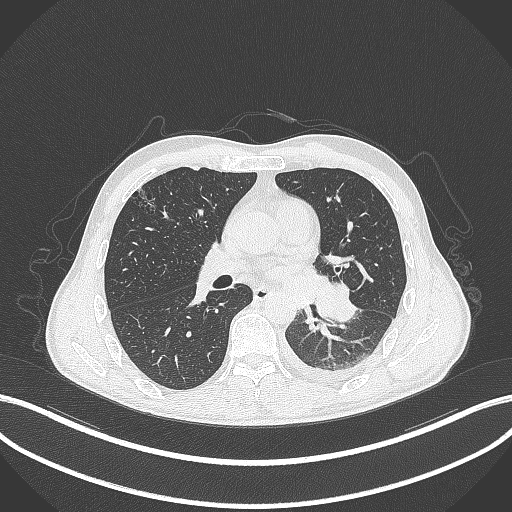
Chest CT, one axial slice; position 167 of 295 along the scan axis; 120 kVp; lung window (W 1500 / L -600 HU); 1 mm slice thickness; 512 × 512 image matrix, field of view 400 × 400 mm. Male patient, age 47 years. From the clinical record (not read from this slice): clinical TNM (as recorded): T3 N1 M1c.
Structures marked on this image (bounding box drawn by a radiologist):
- lung tumour (recorded histology: small cell carcinoma): bounding box [x1, y1, x2, y2] px = [311, 279, 360, 325]